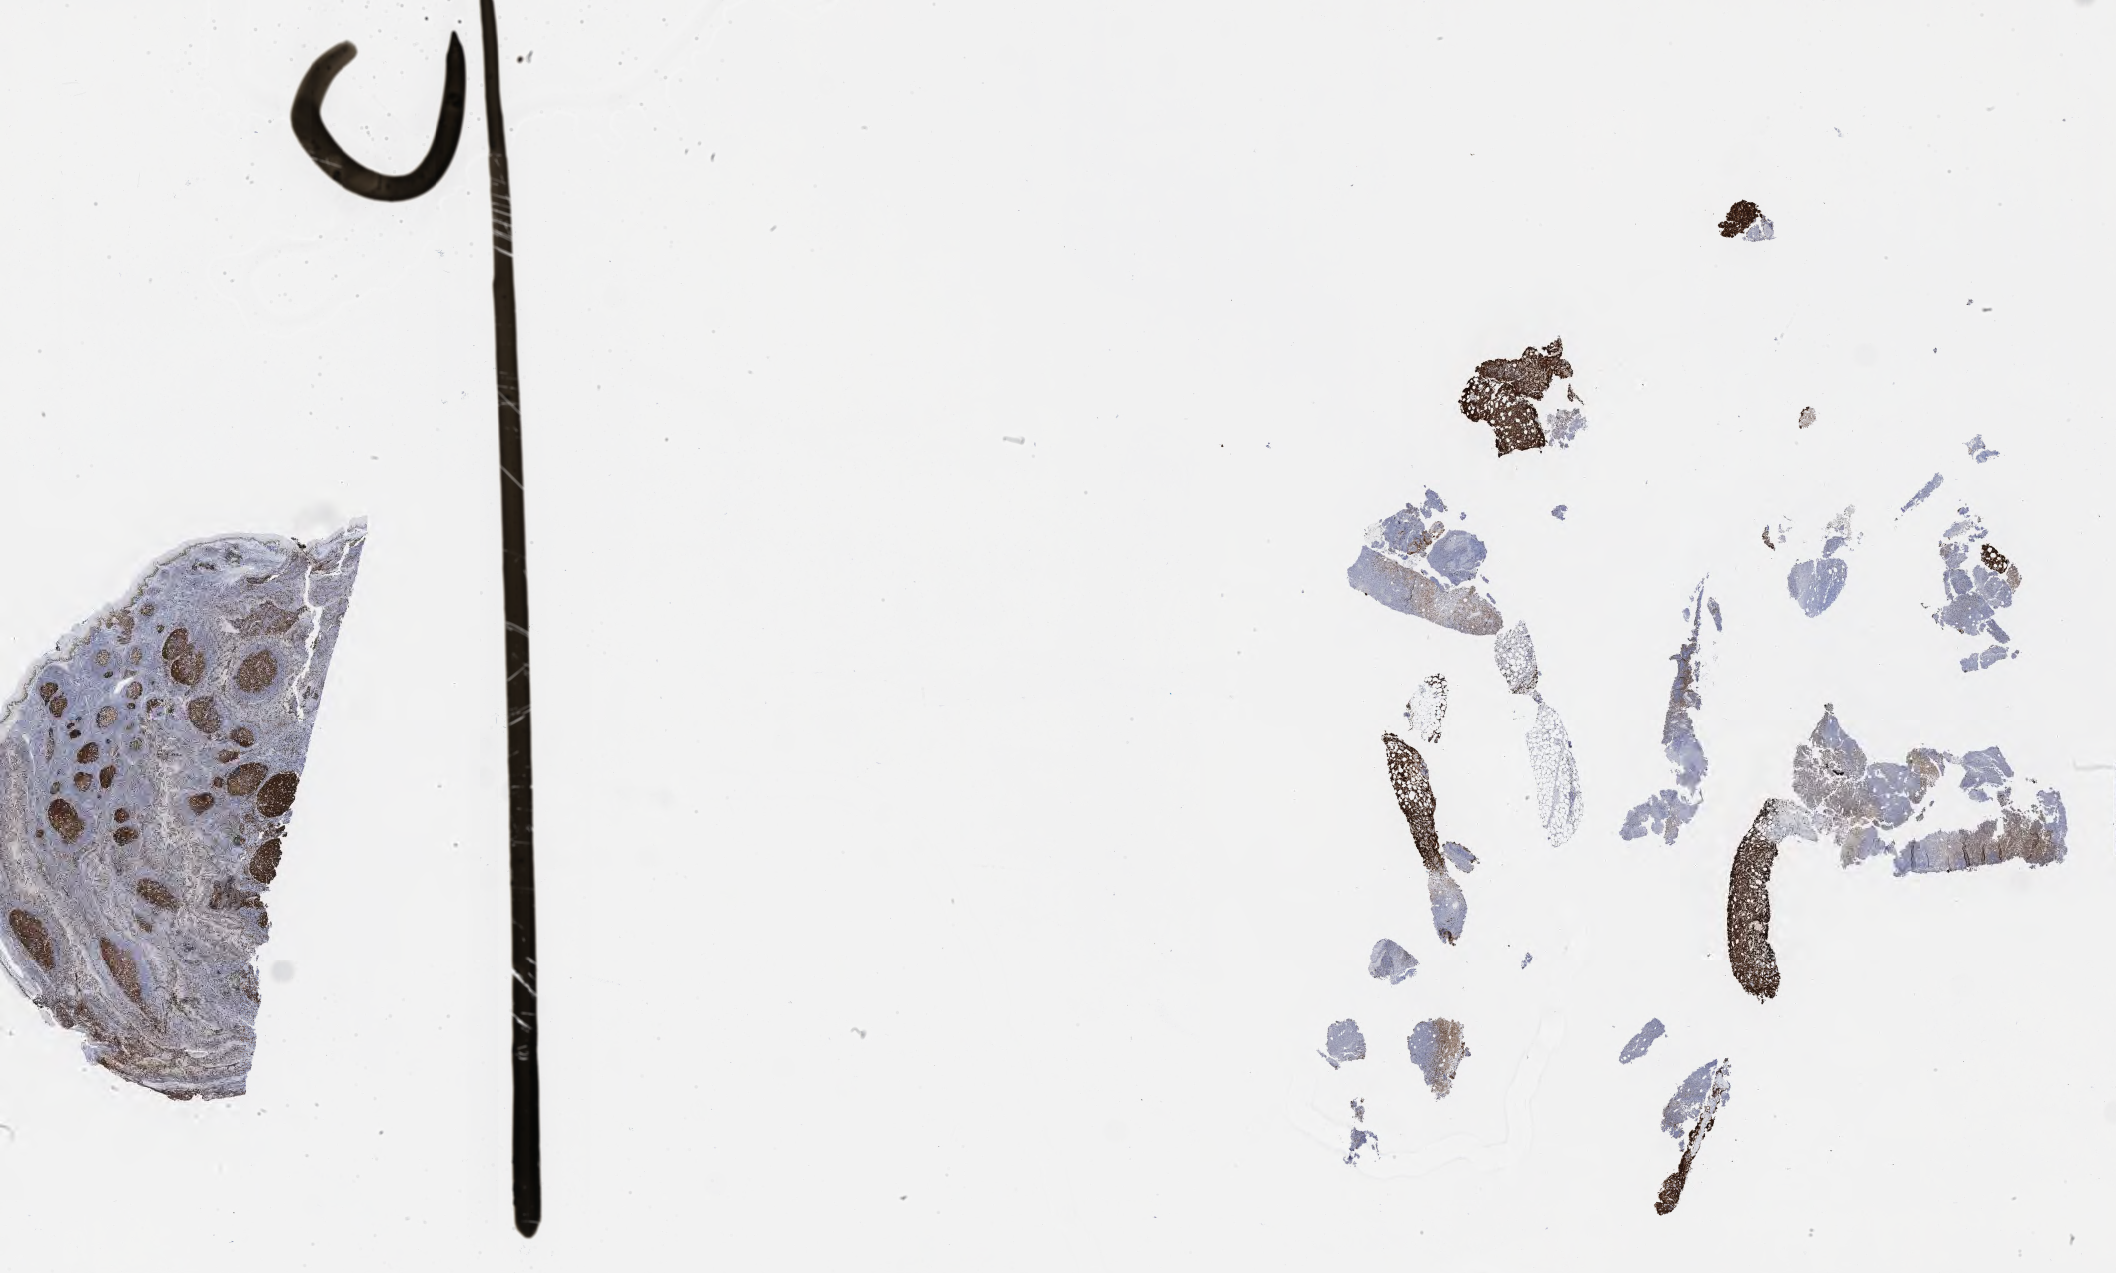
Whole-slide image, immunohistochemical stain for Ki-67, whole scanned area (about 34.2 x 20.6 mm) shown as a low-resolution overview. Specimen: tumor tissue. Anatomic site: pelvis. Patient female; 64 years old.
Diagnosis: Burkitt lymphoma, NOS.